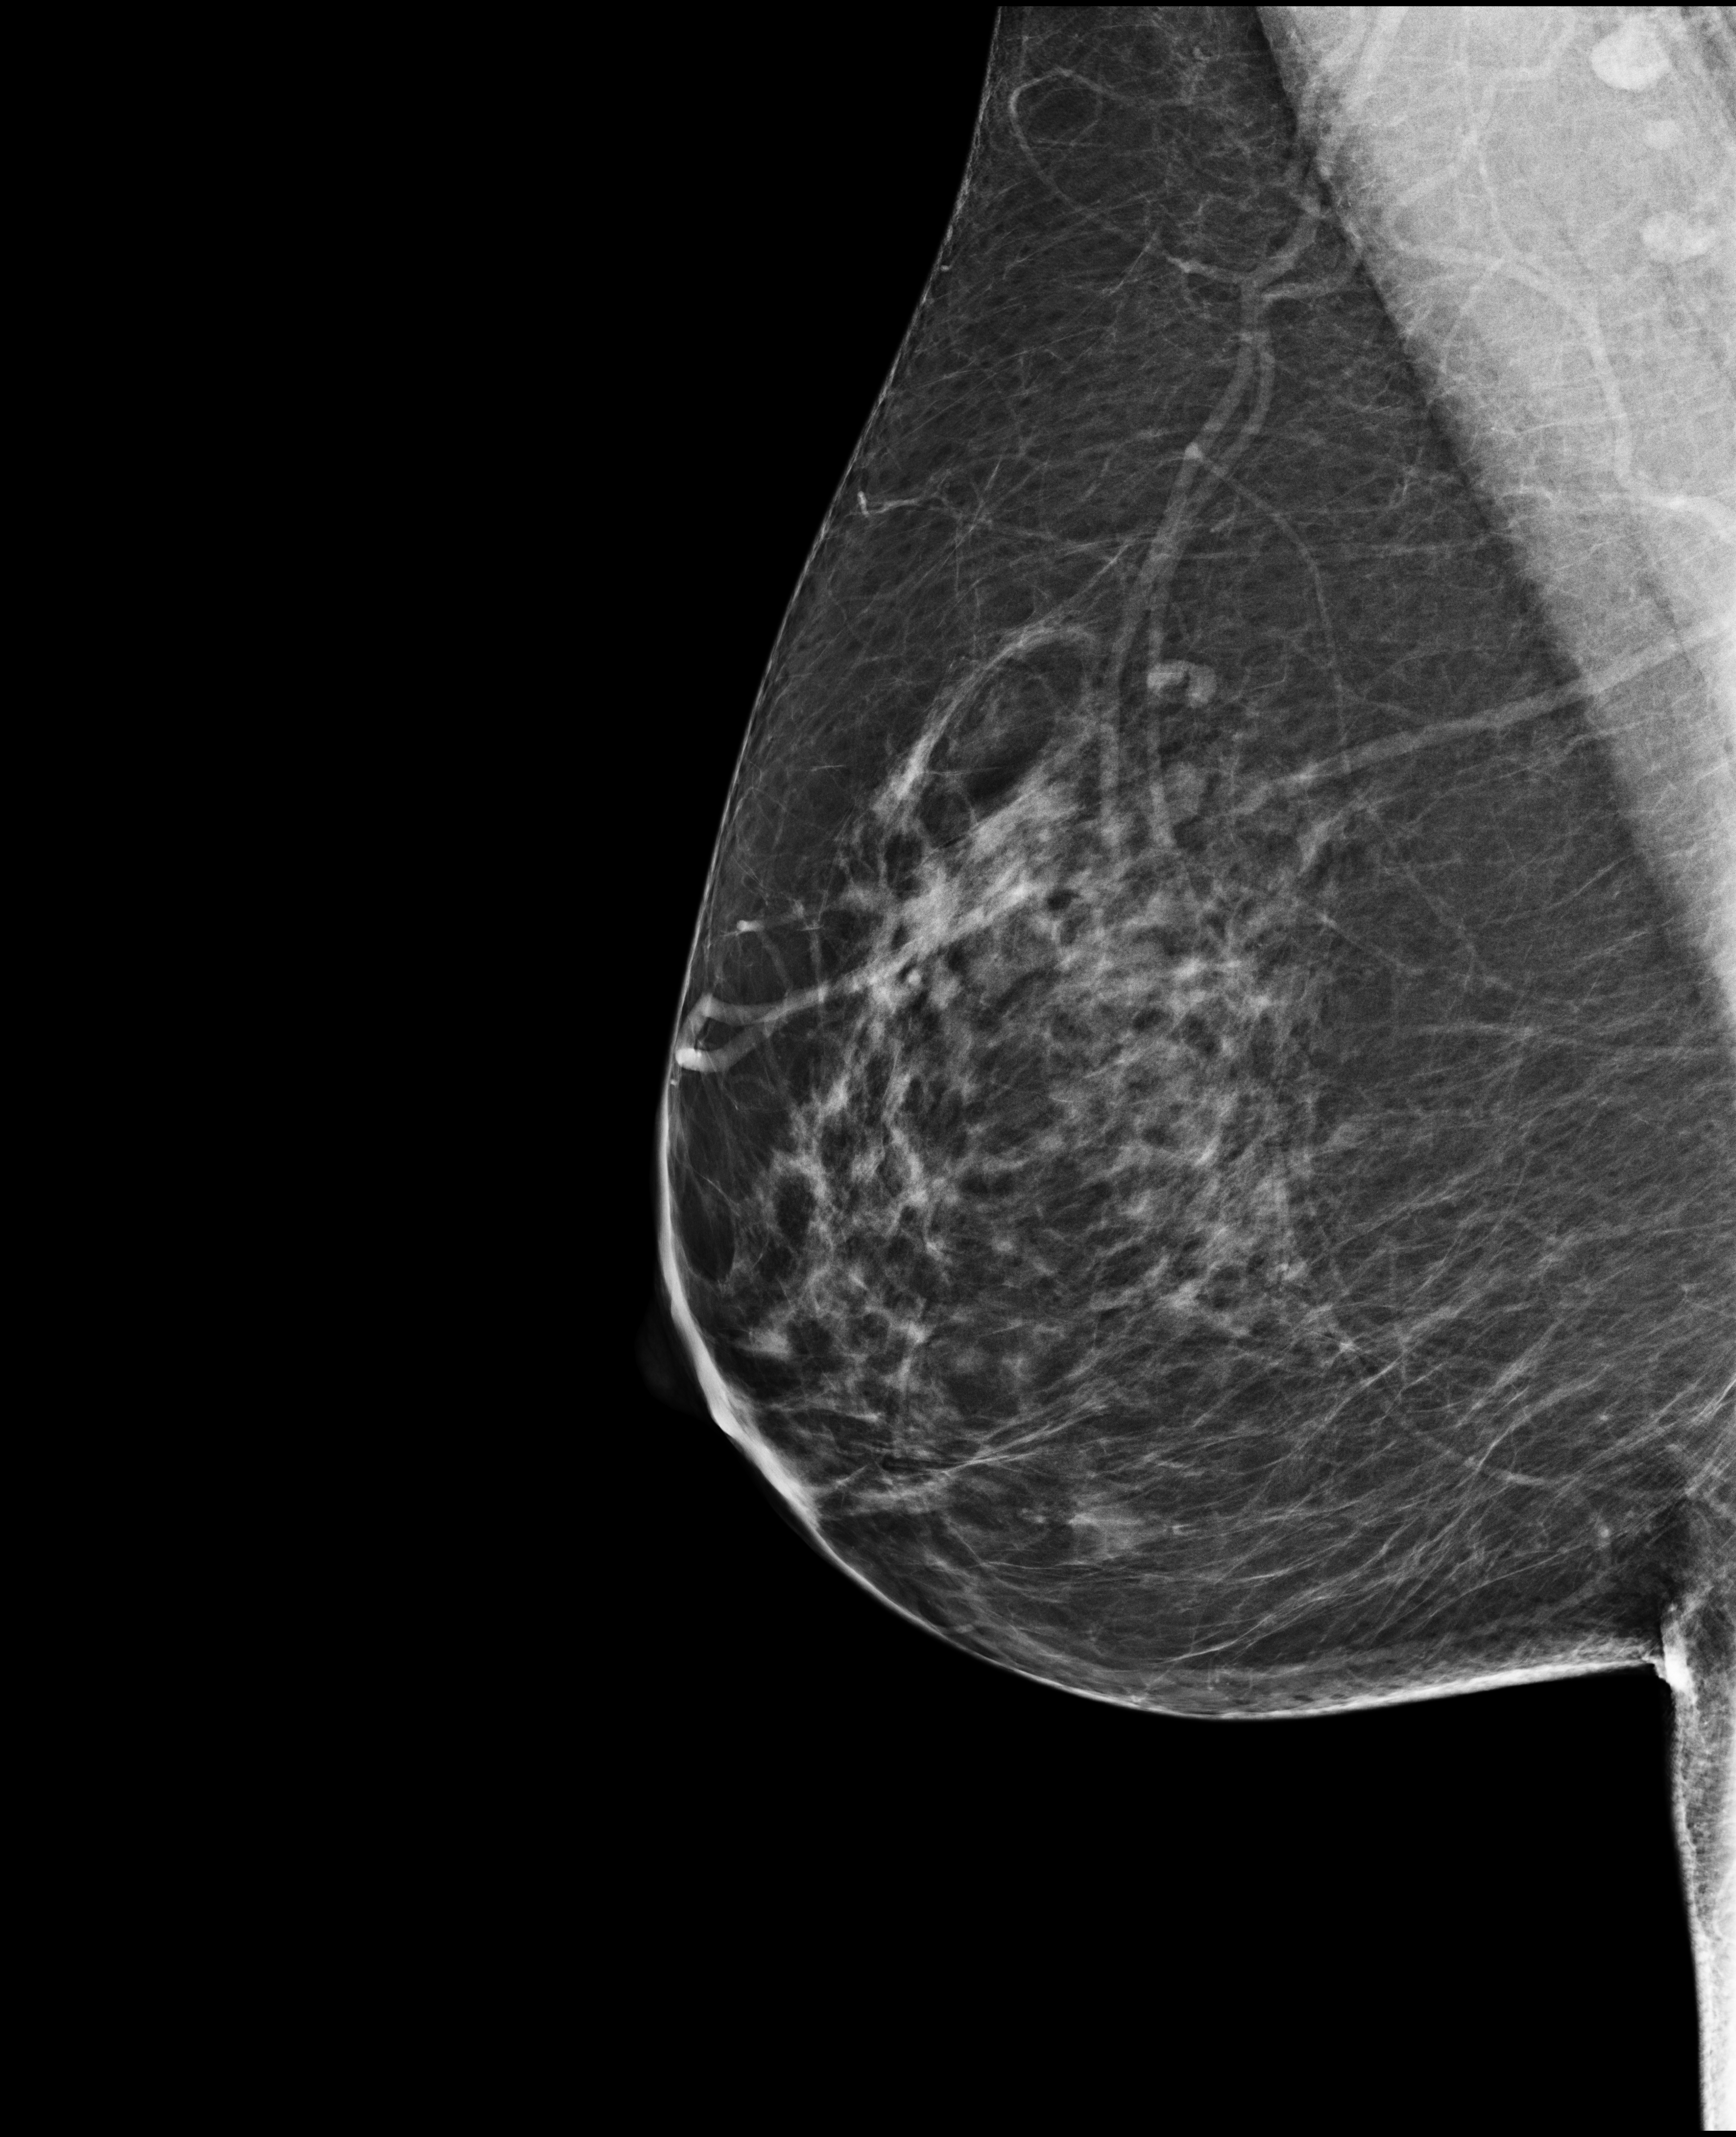
Digital mammogram (FFDM), right breast, MLO view, annual screening mammography examination, system: Selenia Dimensions. Patient aged 59 years (female).
Final BI-RADS assessment for this screening round (tomosynthesis exam, both breasts): category 1.